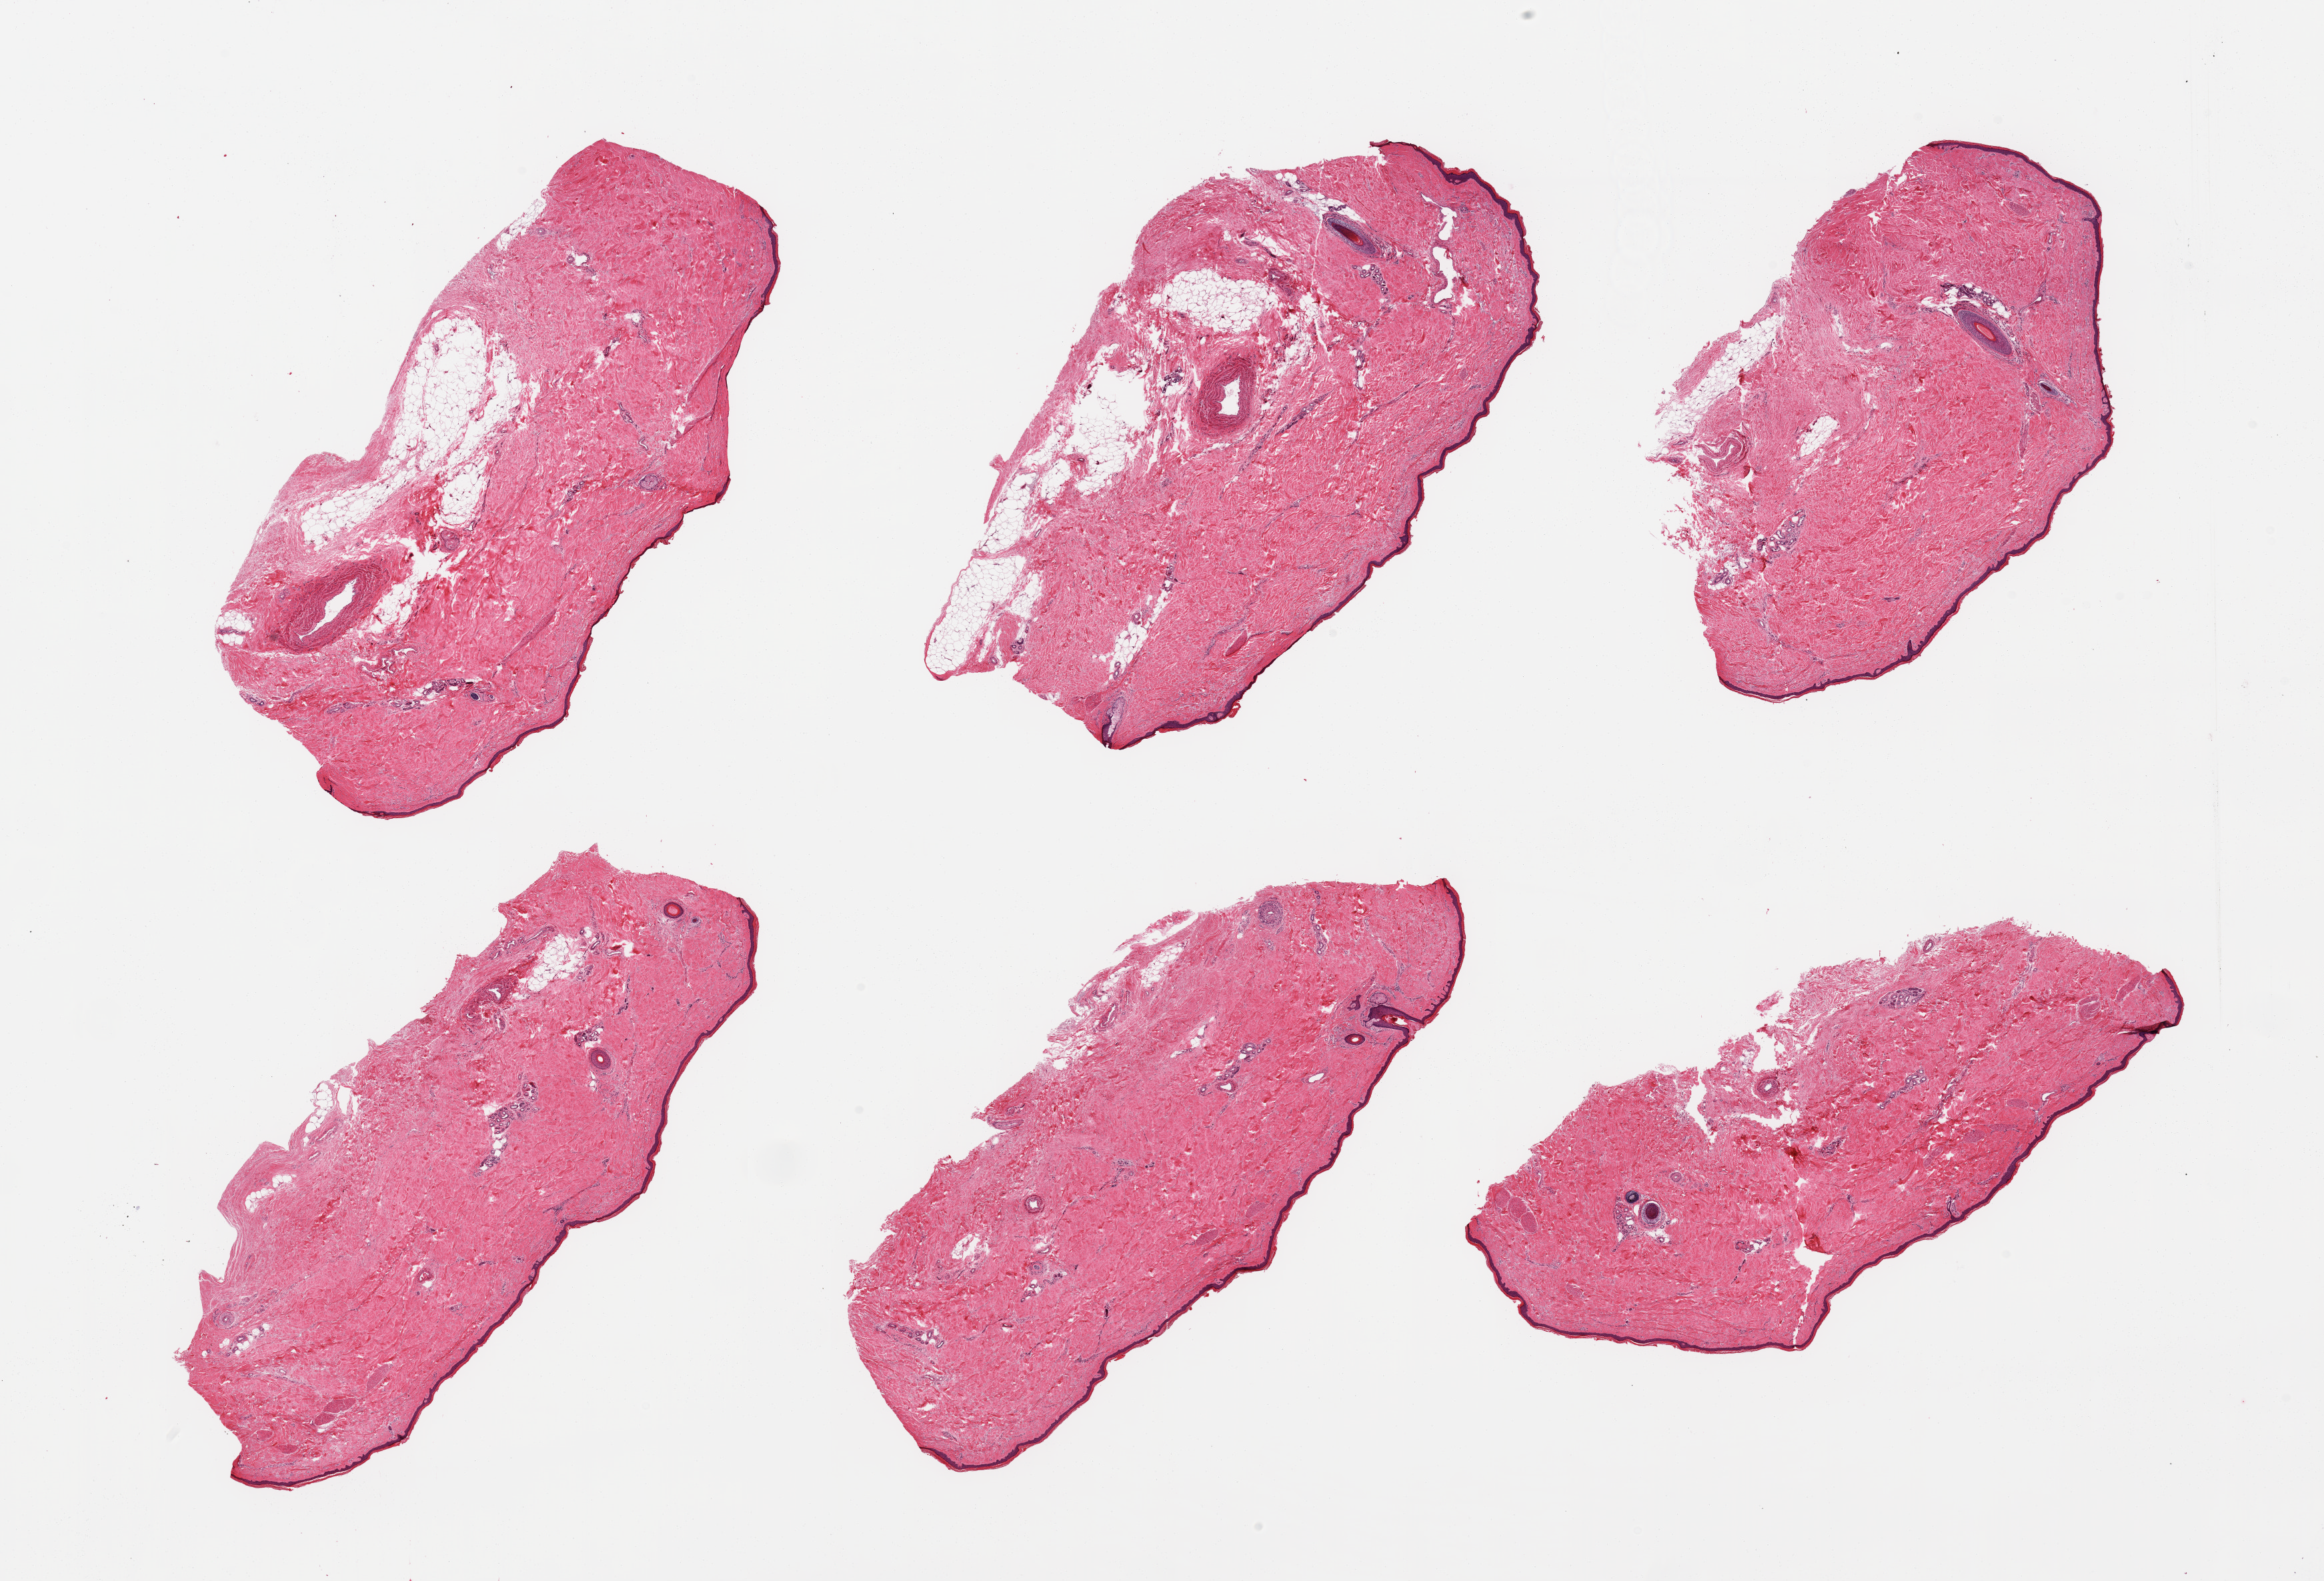
Digitized haematoxylin and eosin-stained section, low-resolution overview of the scanned area, about 27.6 x 18.8 mm (slide scanned at 20x). PAXgene-fixed paraffin-embedded (PFPE) section. Section of skin of lower leg (target tissue). Donor tissue sample. Donor sex: male.
• pathologist's review note for this sample: 6 pieces; includes from 5-15% internal fat, epidermis measures 33 microns, solar elastosis